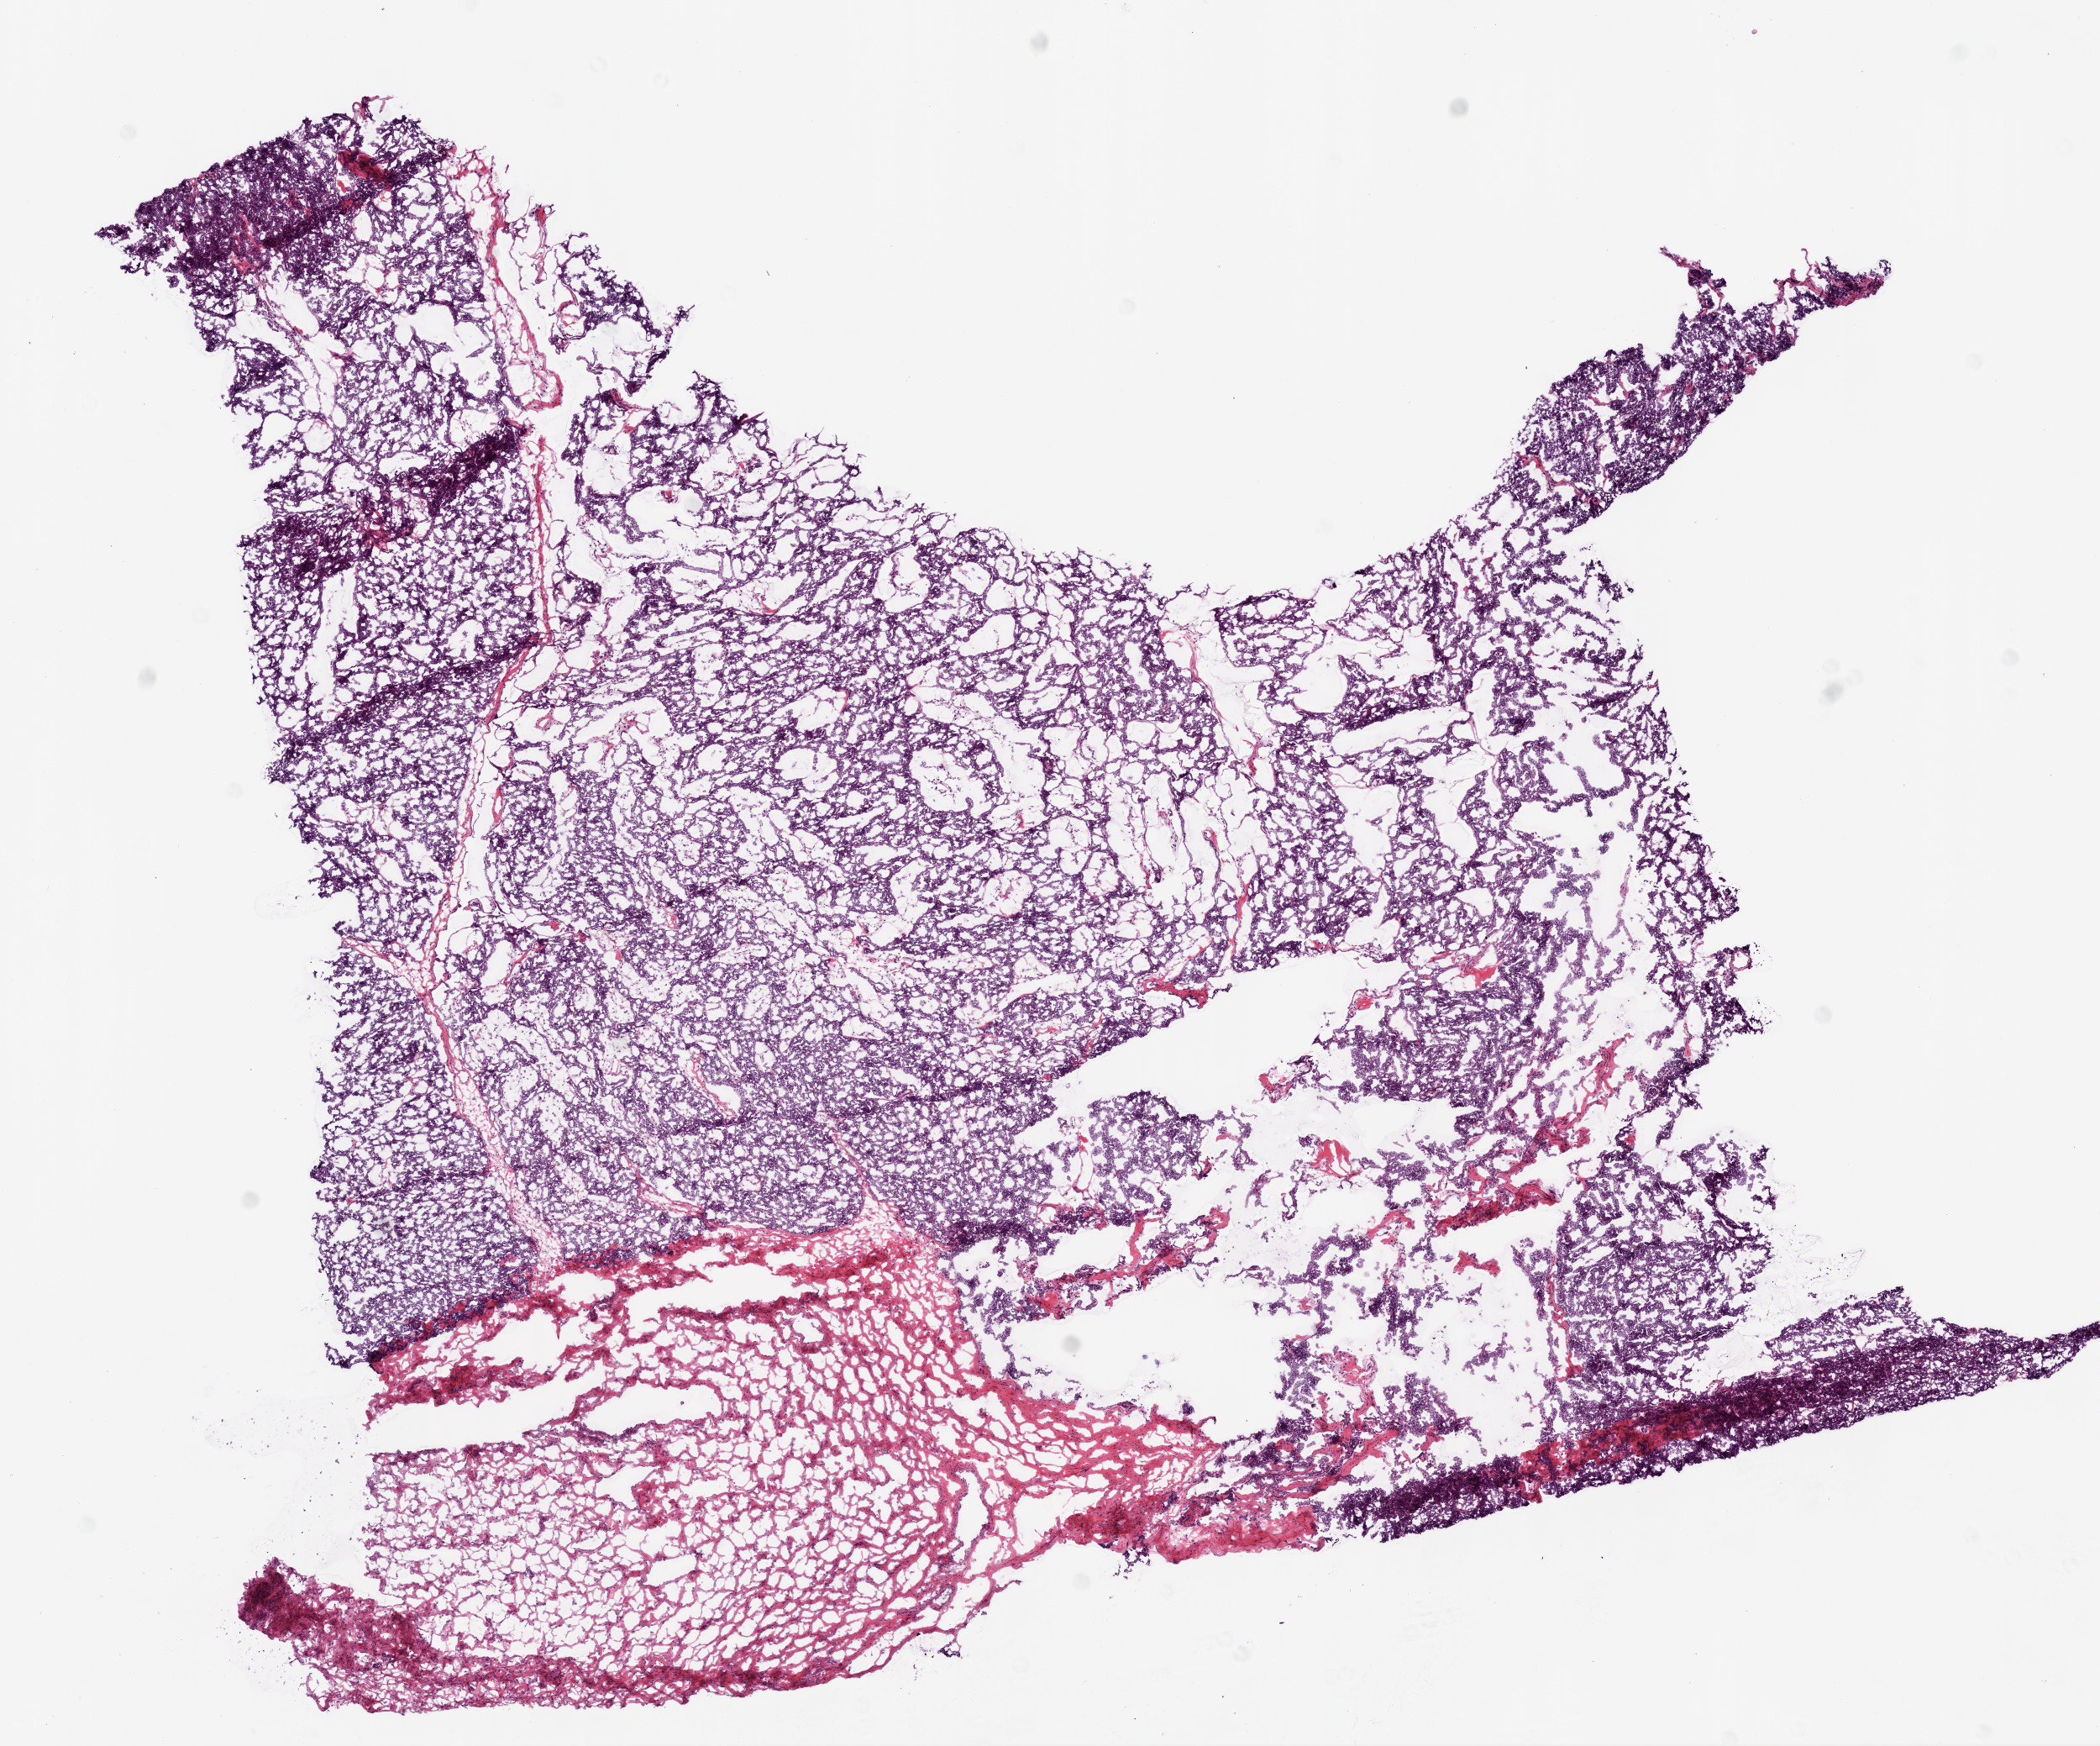
Whole-slide histology image, H&E, shown as a low-resolution overview of the whole scanned area (about 10.0 x 8.3 mm), frozen section from the bottom of the tissue portion, sample: primary tumour, ovary. Female patient; age at initial diagnosis 48 years. Histologic grade: G3 (poorly differentiated). Composition of this section per pathologist review: tumour cells 90%, tumour nuclei 95%, normal cells 0%, stromal cells 10%, necrosis 0%.
• pathologic diagnosis: Serous cystadenocarcinoma, NOS
• FIGO stage: IIIC